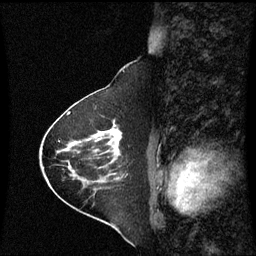
Breast MRI (dynamic contrast-enhanced), one sagittal slice; slice 28 of 60 in the series (ordered by position); dynamic contrast-enhanced series, image 2 of 3 at this slice position (ordered by acquisition); 1.5 T; TE 4.2 ms, TR 8.9 ms; 2 mm slice thickness; 256 × 256 image matrix, field of view 210 × 210 mm. Female patient, age 63 years. From the clinical record (not read from this slice): setting: breast cancer imaged before/during neoadjuvant chemotherapy; receptor status: HR-positive, HER2-negative.
Outlined on this slice (semi-automatic segmentation, software-assisted and operator-edited):
- analysis volume of interest (the breast-tissue region the enhancement analysis was run in; not a lesion): bounding box <88,121,124,163> (left, top, right, bottom; pixels)
- tumour enhancement mask (voxels above the 70 % enhancement threshold inside the analysis volume of interest): <111,130,121,153>